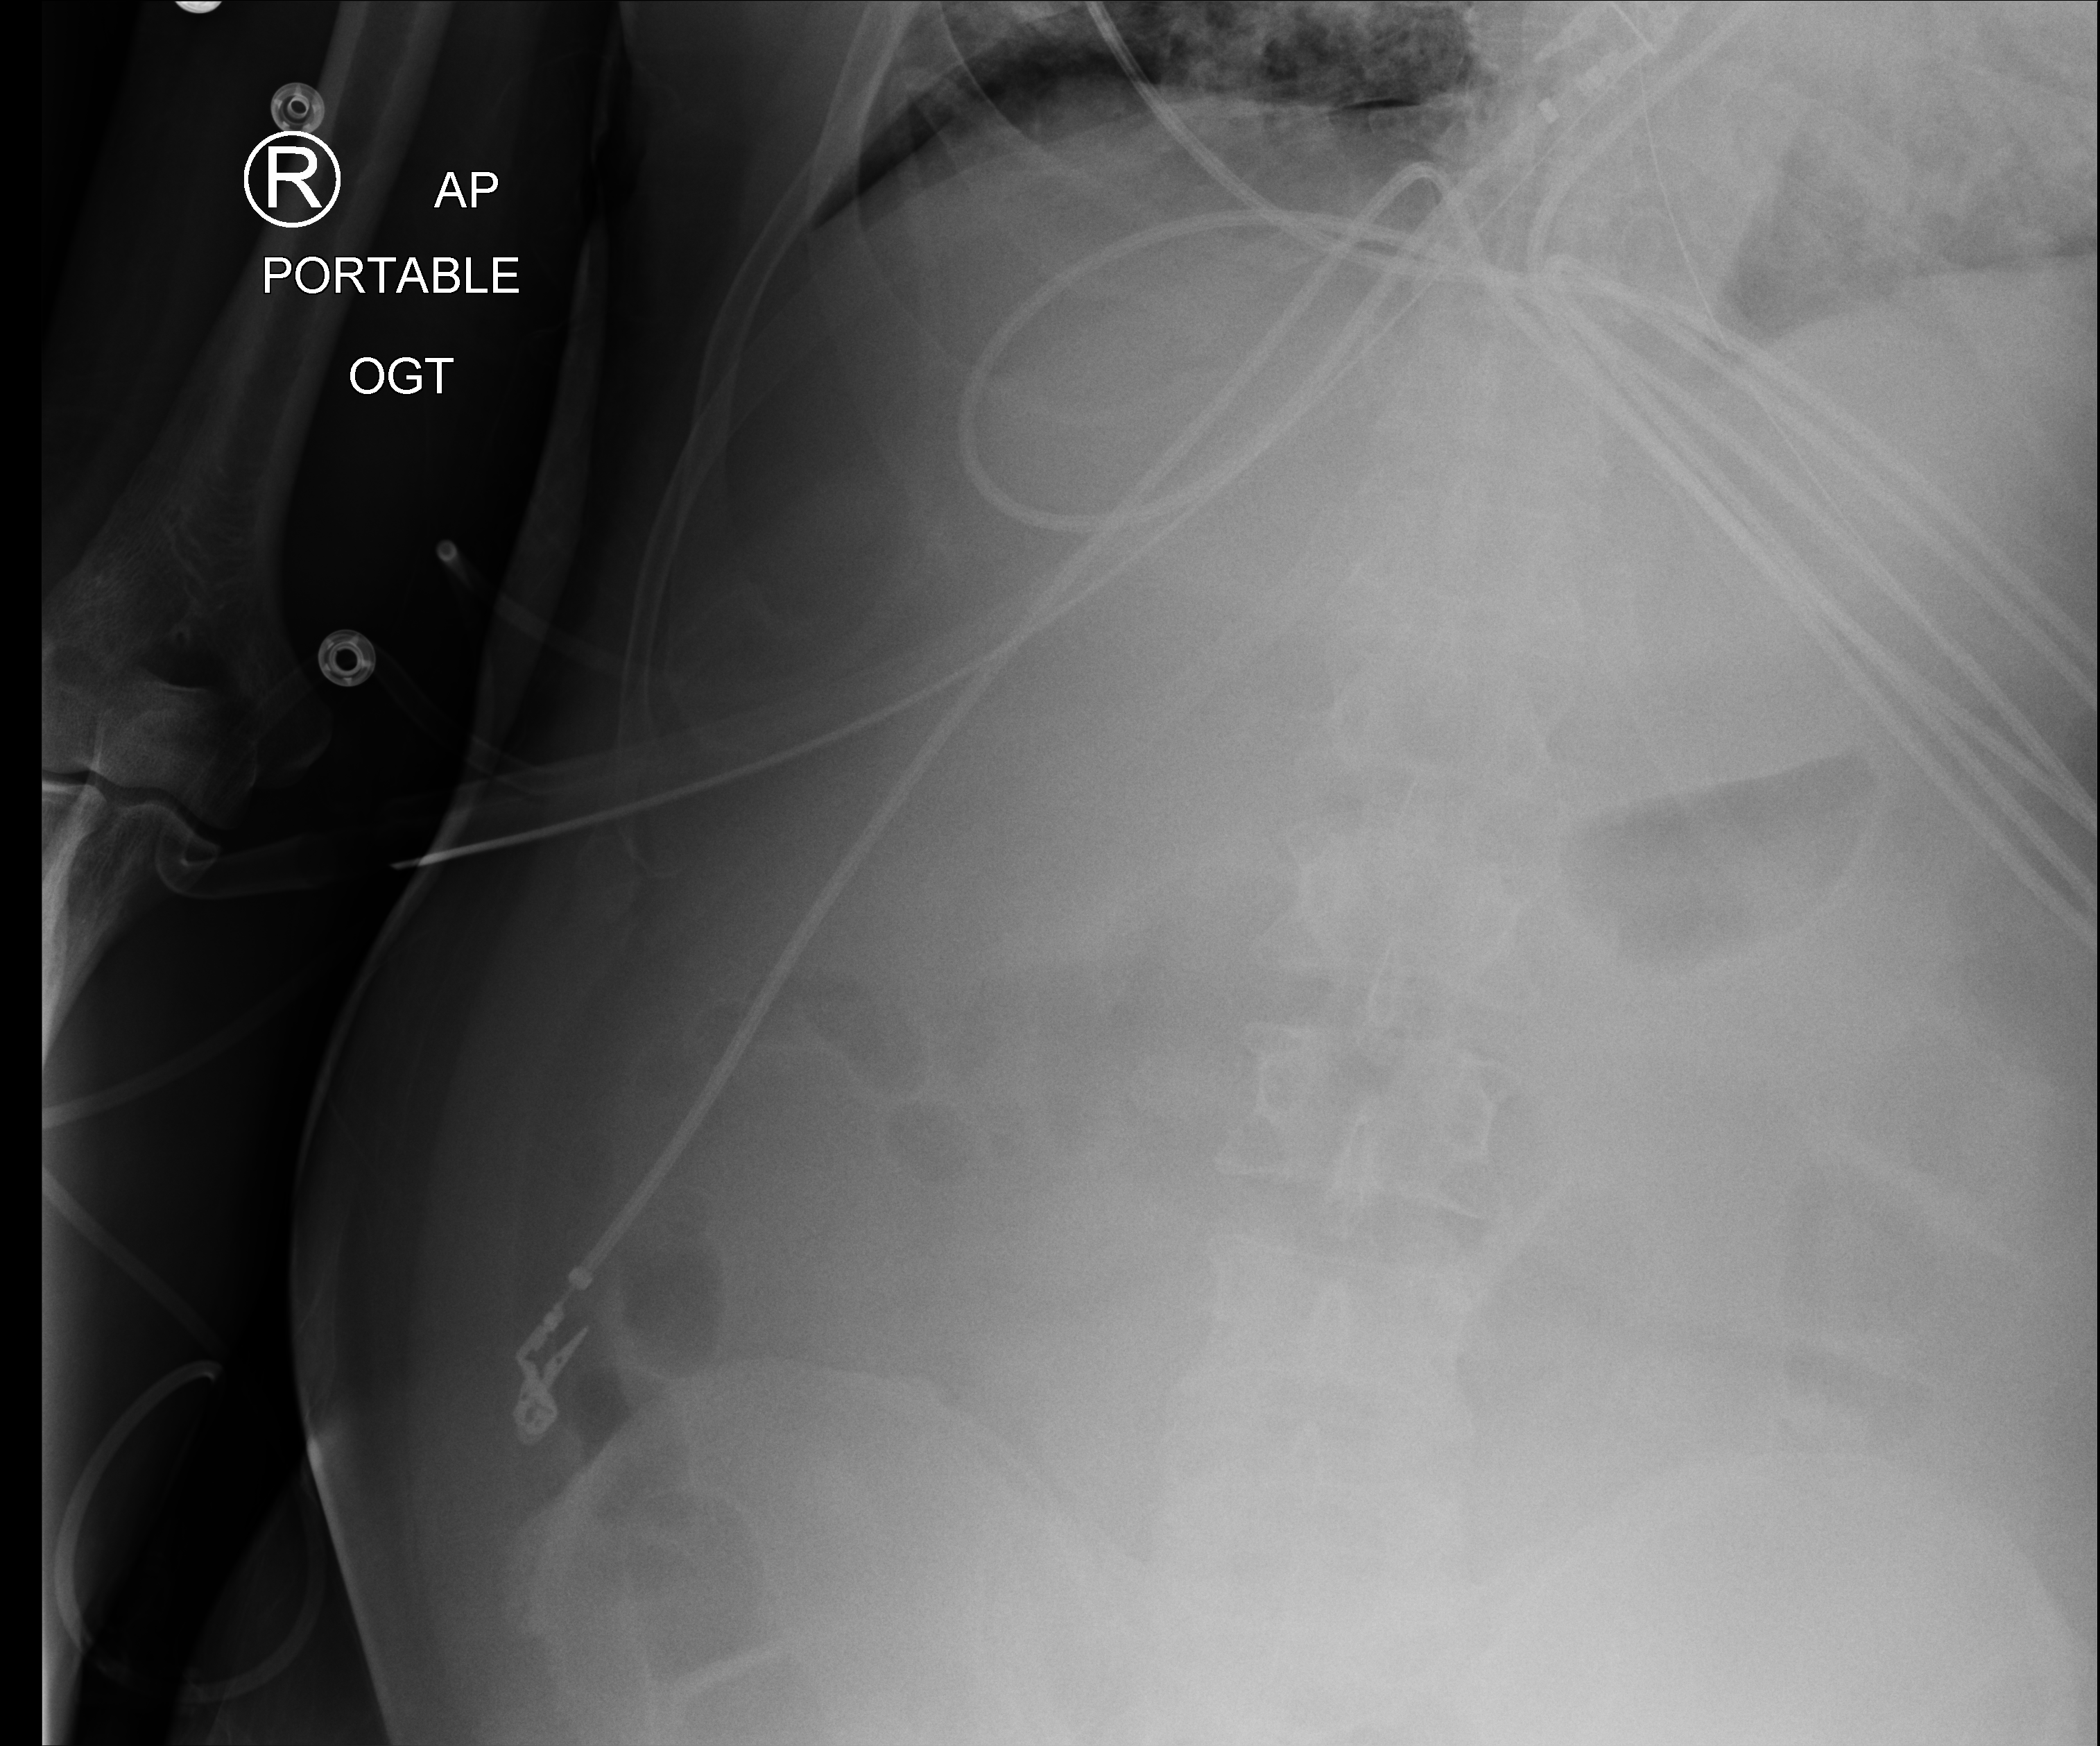
Bedside chest radiograph (computed radiography), anteroposterior (AP) projection. Male patient hospitalised with COVID-19, age 18–59 years.
Hospital-stay facts (about this admission, not read from this image; timing relative to this image not recorded):
- mechanically ventilated during this hospital stay: yes